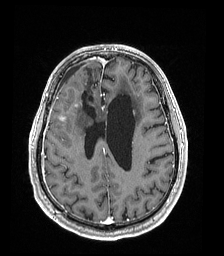
Brain MRI from a brain-tumour surgery series, one axial slice. T1-weighted post-contrast. 224 × 256 image matrix. From the clinical record (not read from this slice): histopathology: Astrocytoma; WHO grade: 4; IDH mutation: yes; tumour location: Right Frontal.
Outlined on this slice (outlined manually by an expert reader):
- previous resection cavity: bounding box <82,67,98,115> (left, top, right, bottom; pixels)